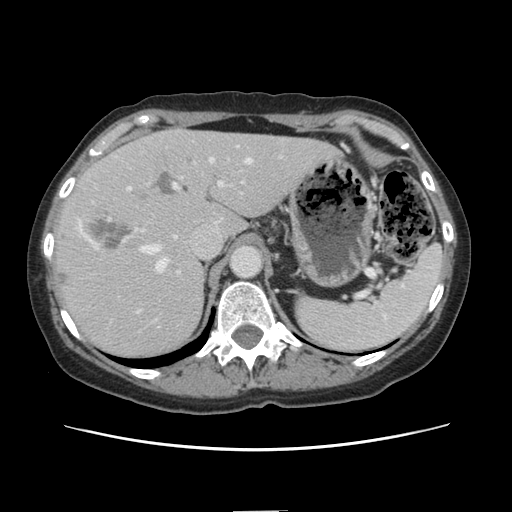
Contrast-enhanced abdominal CT, one axial slice; slice 101 of 141 in the series (ordered by position); 120 kVp; intravenous contrast given; soft-tissue window (W 400 / L 40 HU); 512 × 512 image matrix, field of view 350 × 350 mm. Female patient, age 63 years. From the clinical record (not read from this slice): diagnosis: colorectal cancer liver metastases, imaged before liver resection; multiple liver metastases: yes; largest metastasis: 3.2 cm; disease in both lobes: yes.
Annotated regions visible in this slice (outlined manually by an expert reader):
- hepatic veins: bounding box <142,158,251,271> (left, top, right, bottom; pixels)
- liver: <53,130,335,358>
- planned liver remnant (the part of the liver to remain after resection): <185,131,335,238>
- portal vein (with intrahepatic branches): <127,181,224,273>